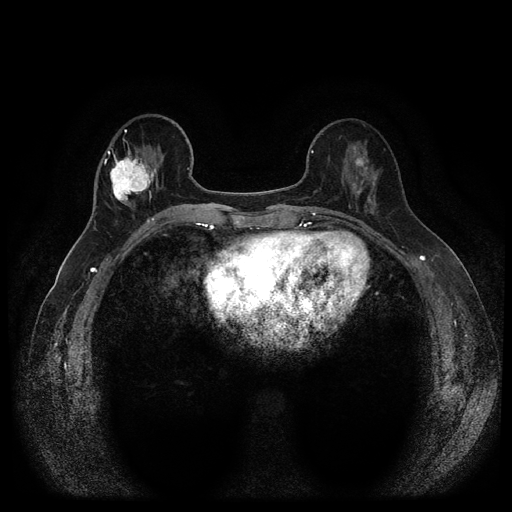
Breast MRI (dynamic contrast-enhanced, multi-phase), one axial slice; slice 38 of 116 in the series (ordered by position); dynamic contrast-enhanced series, time point 2 of 5 at this slice position (early post-contrast); 1.5 T; TE 2.6 ms, TR 5.4 ms; 512 × 512 image matrix, field of view 340 × 340 mm. Patient: female, 56 years.
Outlined on this slice (semi-automatically segmented with operator editing):
- breast lesion (labelled benign in the annotation): bounding box <350,141,370,199> (left, top, right, bottom; pixels)
- breast lesion (labelled 'tumour' in the annotation; benign lesions carry a separate 'benign' label): <105,149,158,207>